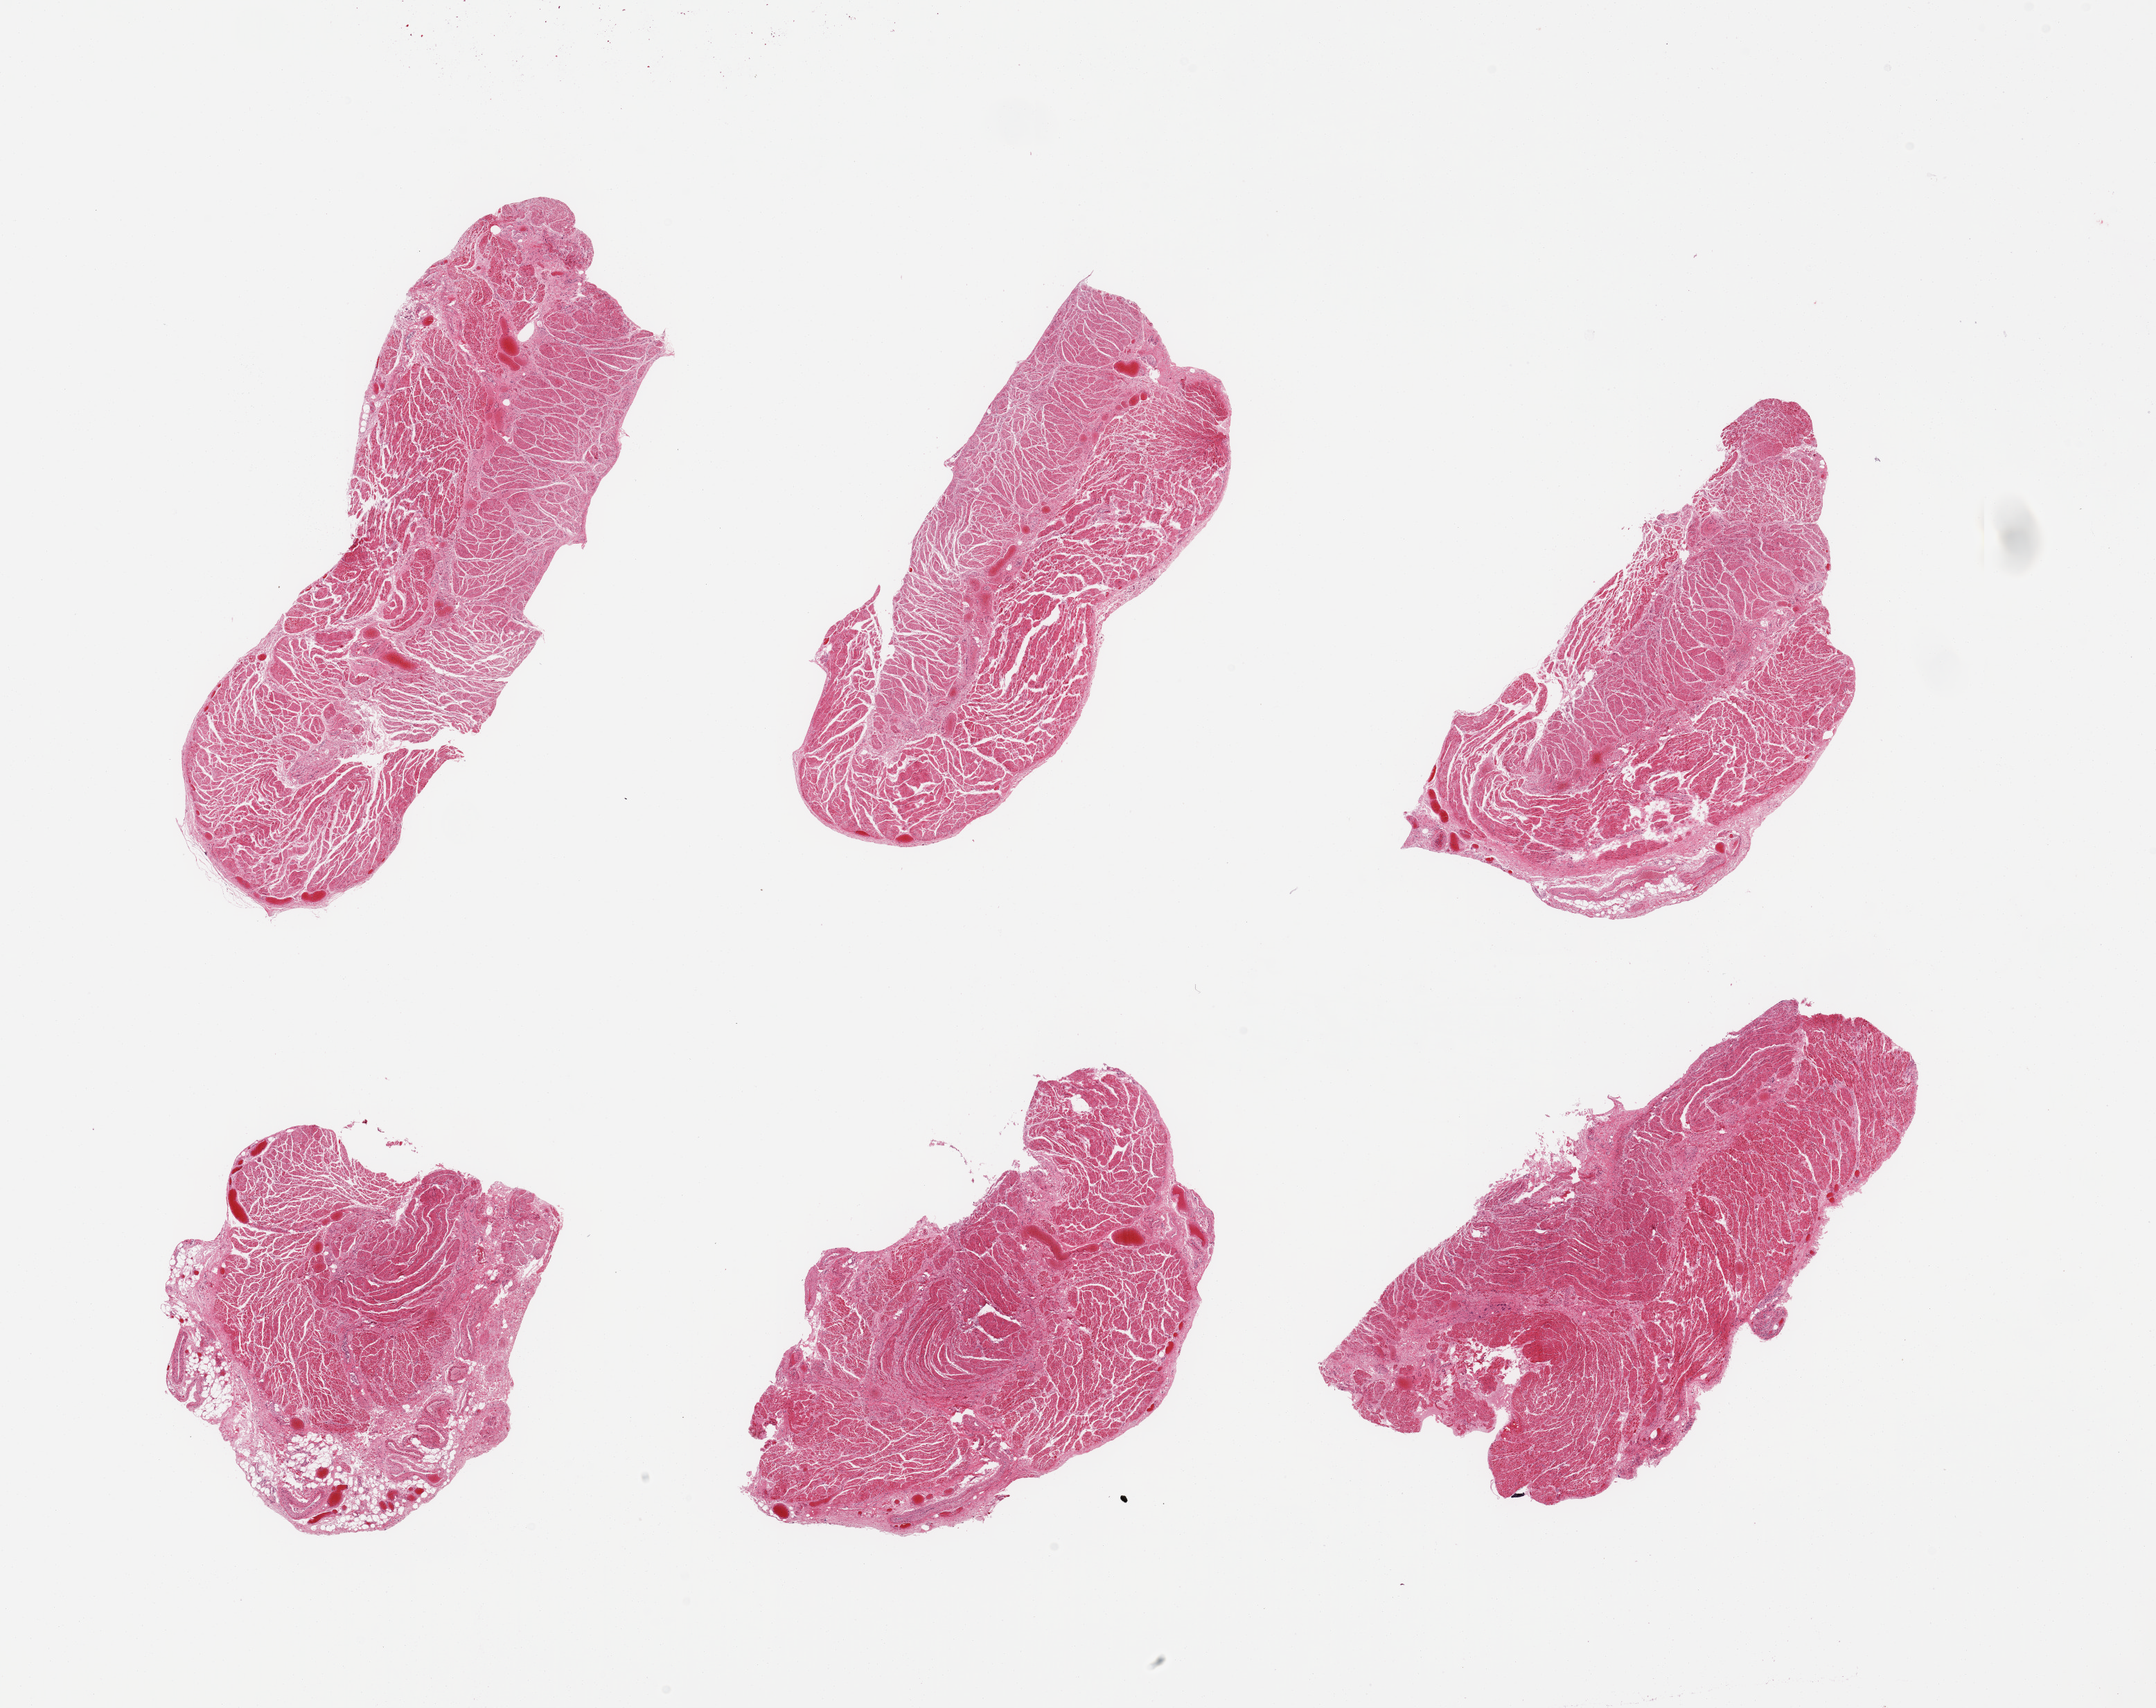
Haematoxylin and eosin whole-slide image — shown as a low-resolution overview of the whole scanned area (about 24.6 x 19.5 mm), PAXgene-fixed, paraffin-embedded tissue, sampled site (target tissue): gastroesophageal junction, donor tissue sample. Male donor.
Review note (as recorded): 6 pieces; well dissected.